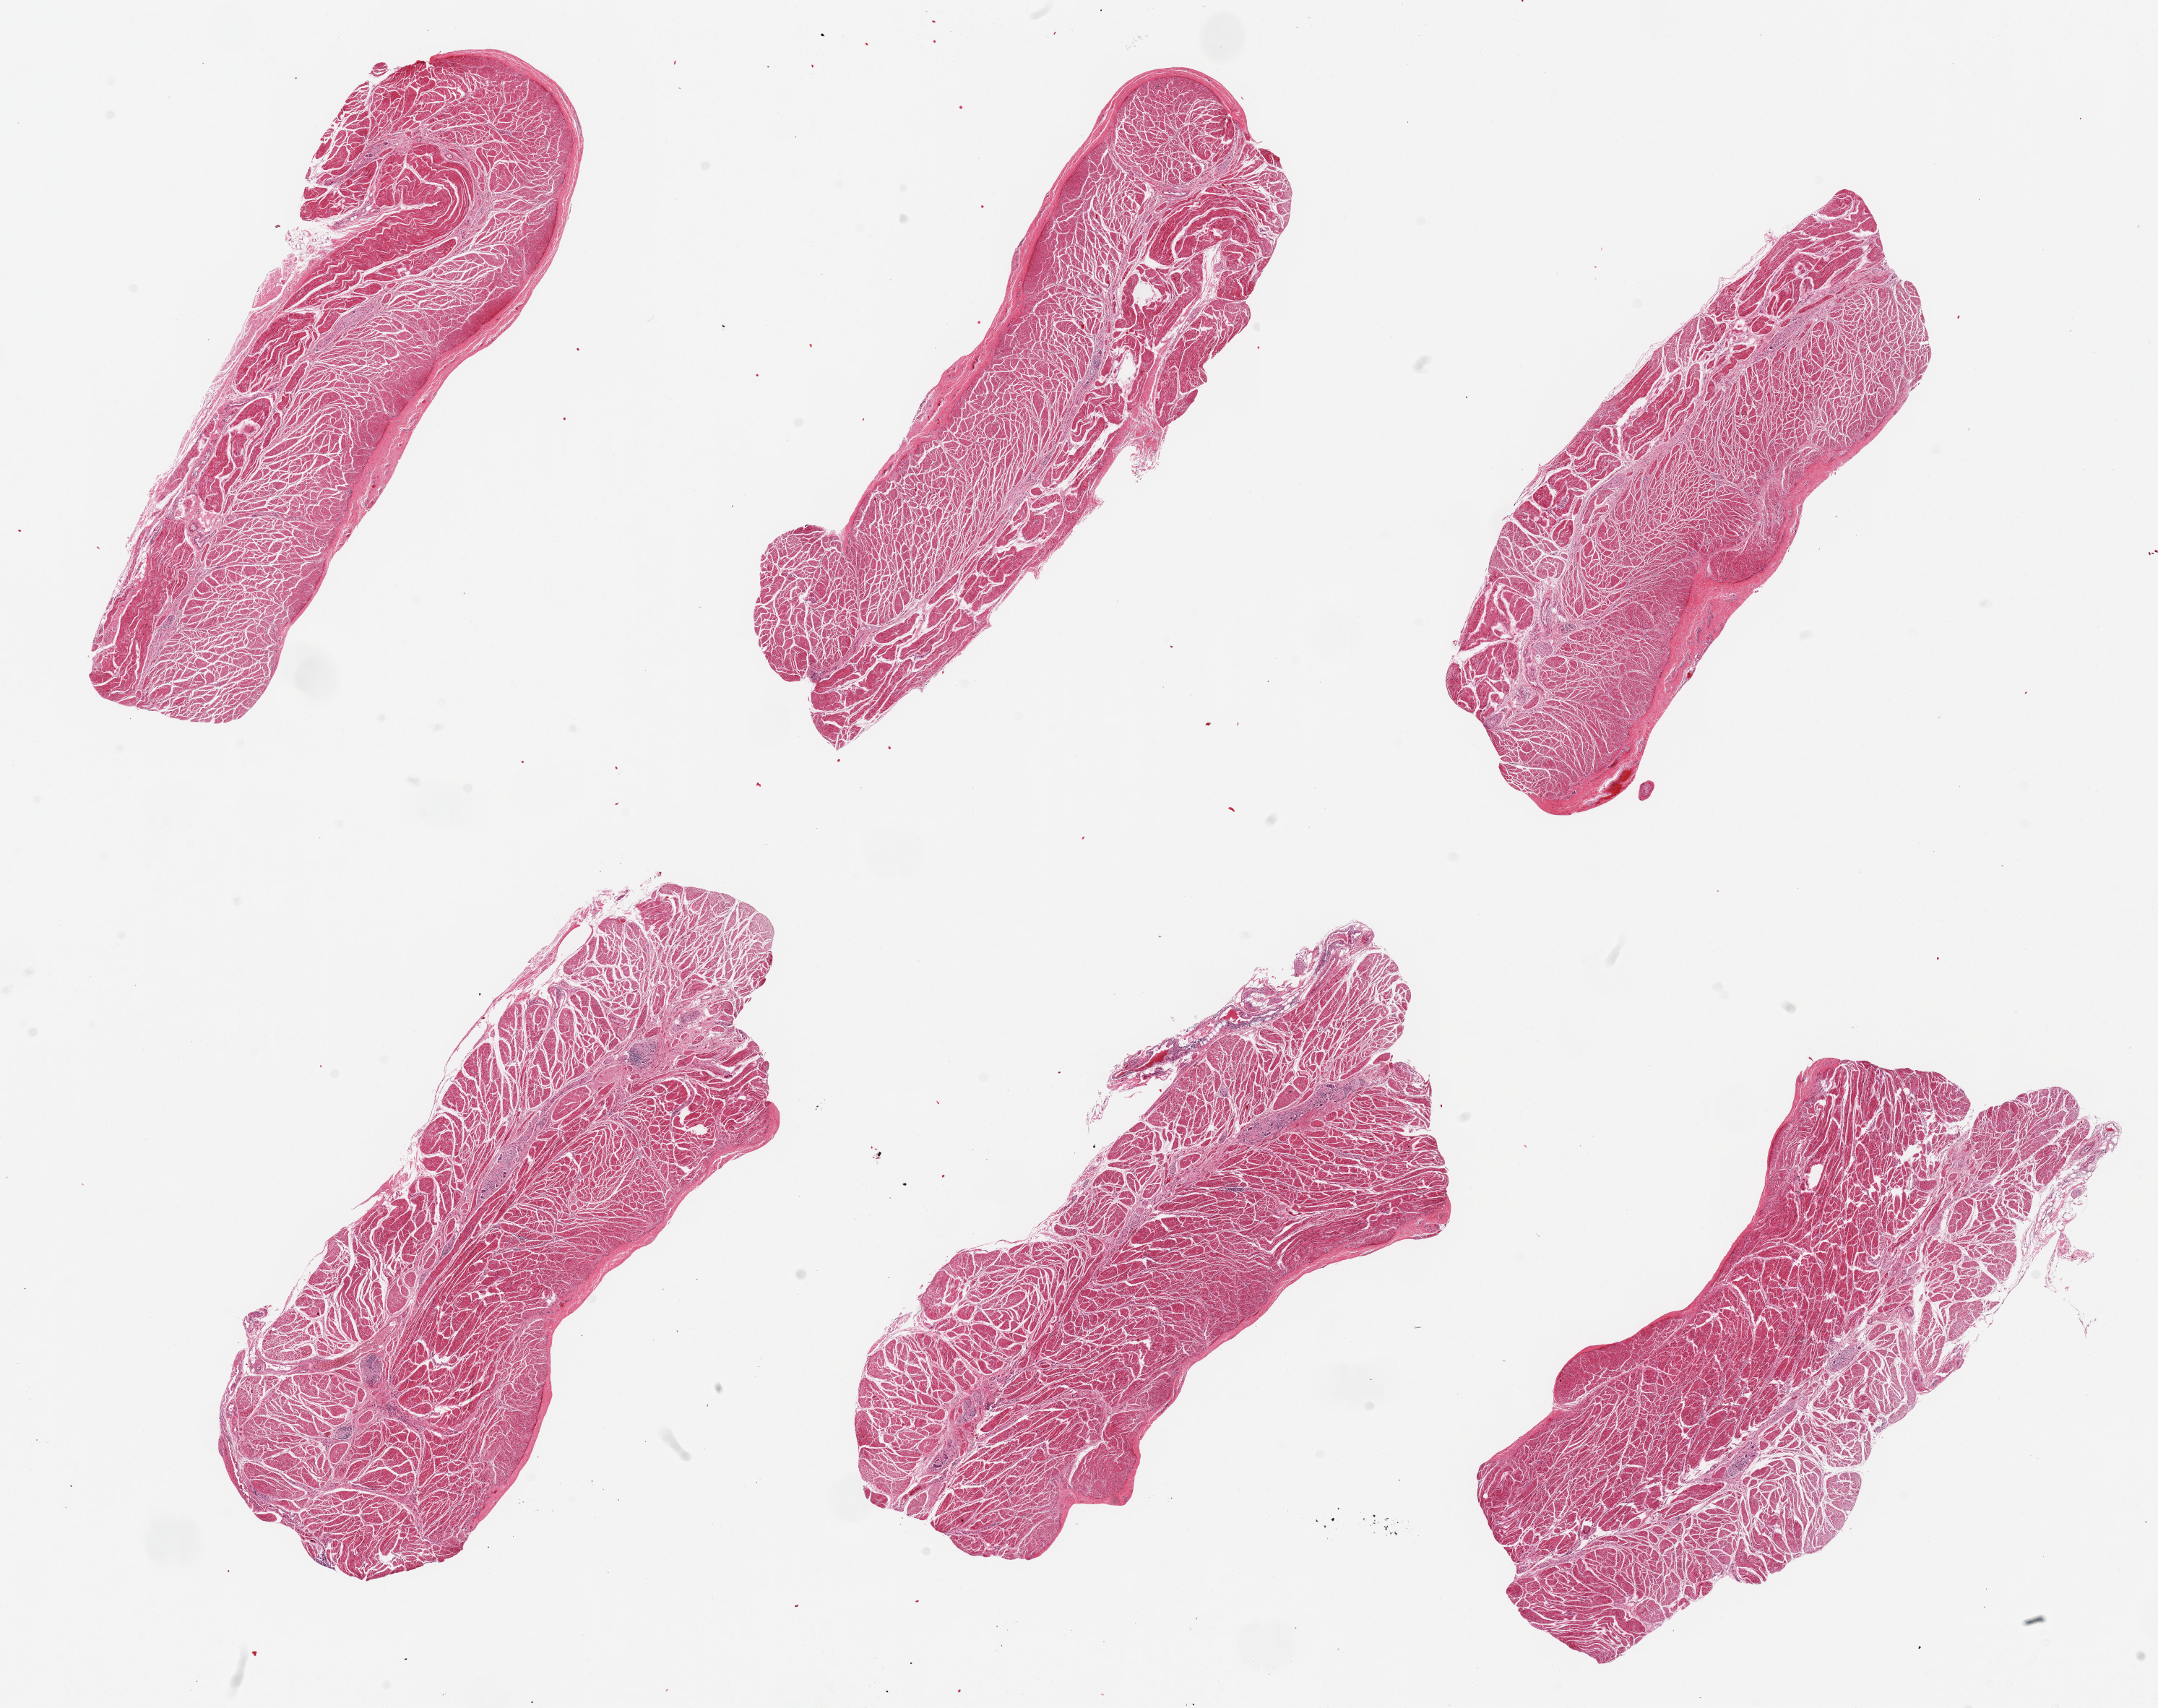
Whole-slide image, H&E stain, low-resolution overview of the scanned area, about 23.6 x 18.7 mm. PAXgene-fixed, paraffin-embedded tissue. Target tissue: gastroesophageal junction. Donor tissue sample. Donor sex: male.
- review note (as recorded): 6 pieces, all muscularis; good specimens